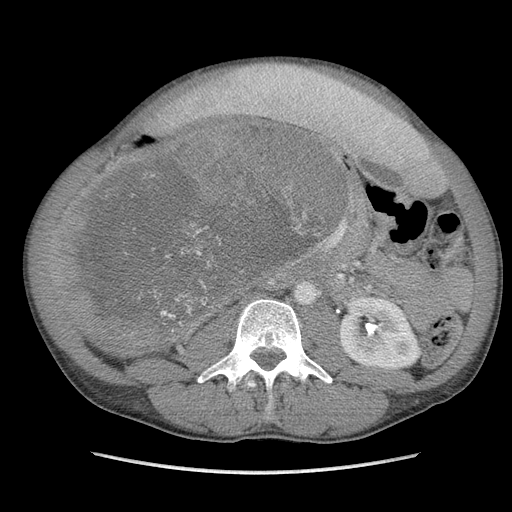
Contrast-enhanced abdominal CT, one axial slice; slice 50 of 115 in the series (ordered by position); soft-tissue window (W 400 / L 40 HU); 5 mm slice thickness; 512 × 512 image matrix, field of view 360 × 360 mm. Male patient. Case-level facts recorded for this patient, not image findings: diagnosis: adrenocortical carcinoma; tumour side: right adrenal; Ki-67 index: 13 %; stage (as recorded): 3.
Annotated regions visible in this slice (semi-automatically segmented with operator editing):
- mass: bounding box [x1, y1, x2, y2] px = [67, 124, 338, 347]